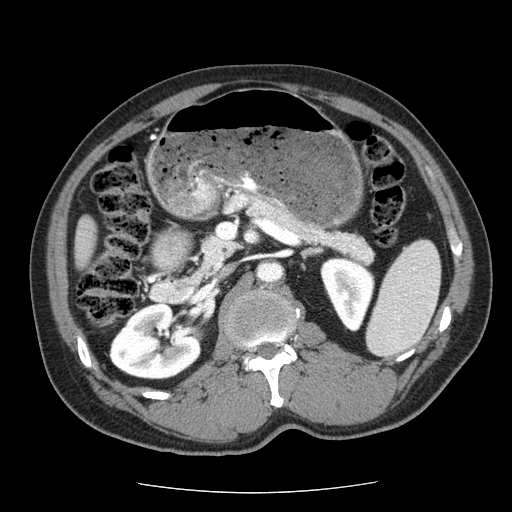
Contrast-enhanced abdominal CT (liver protocol), one axial slice. Reconstruction kernel STANDARD. Soft-tissue window (W 400 / L 40 HU). 2.5 mm slice thickness. 512 × 512 image matrix, field of view 360 × 360 mm. Case-level facts recorded for this patient, not image findings: diagnosis: hepatocellular carcinoma (patient treated with transarterial chemoembolisation; whether this scan precedes or follows treatment is not stated here); TNM stage (as recorded): Stage-IIIA; Child-Pugh class: A; tumour differentiation: well differentiated; tumour size: 8 cm.
Annotated regions visible in this slice (semi-automatic segmentation, software-assisted and operator-edited):
- liver parenchyma outside the tumour (the mass and vessels are separate outlines, so this box may not span the whole liver): box from (x=74, y=216) to (x=96, y=268) px